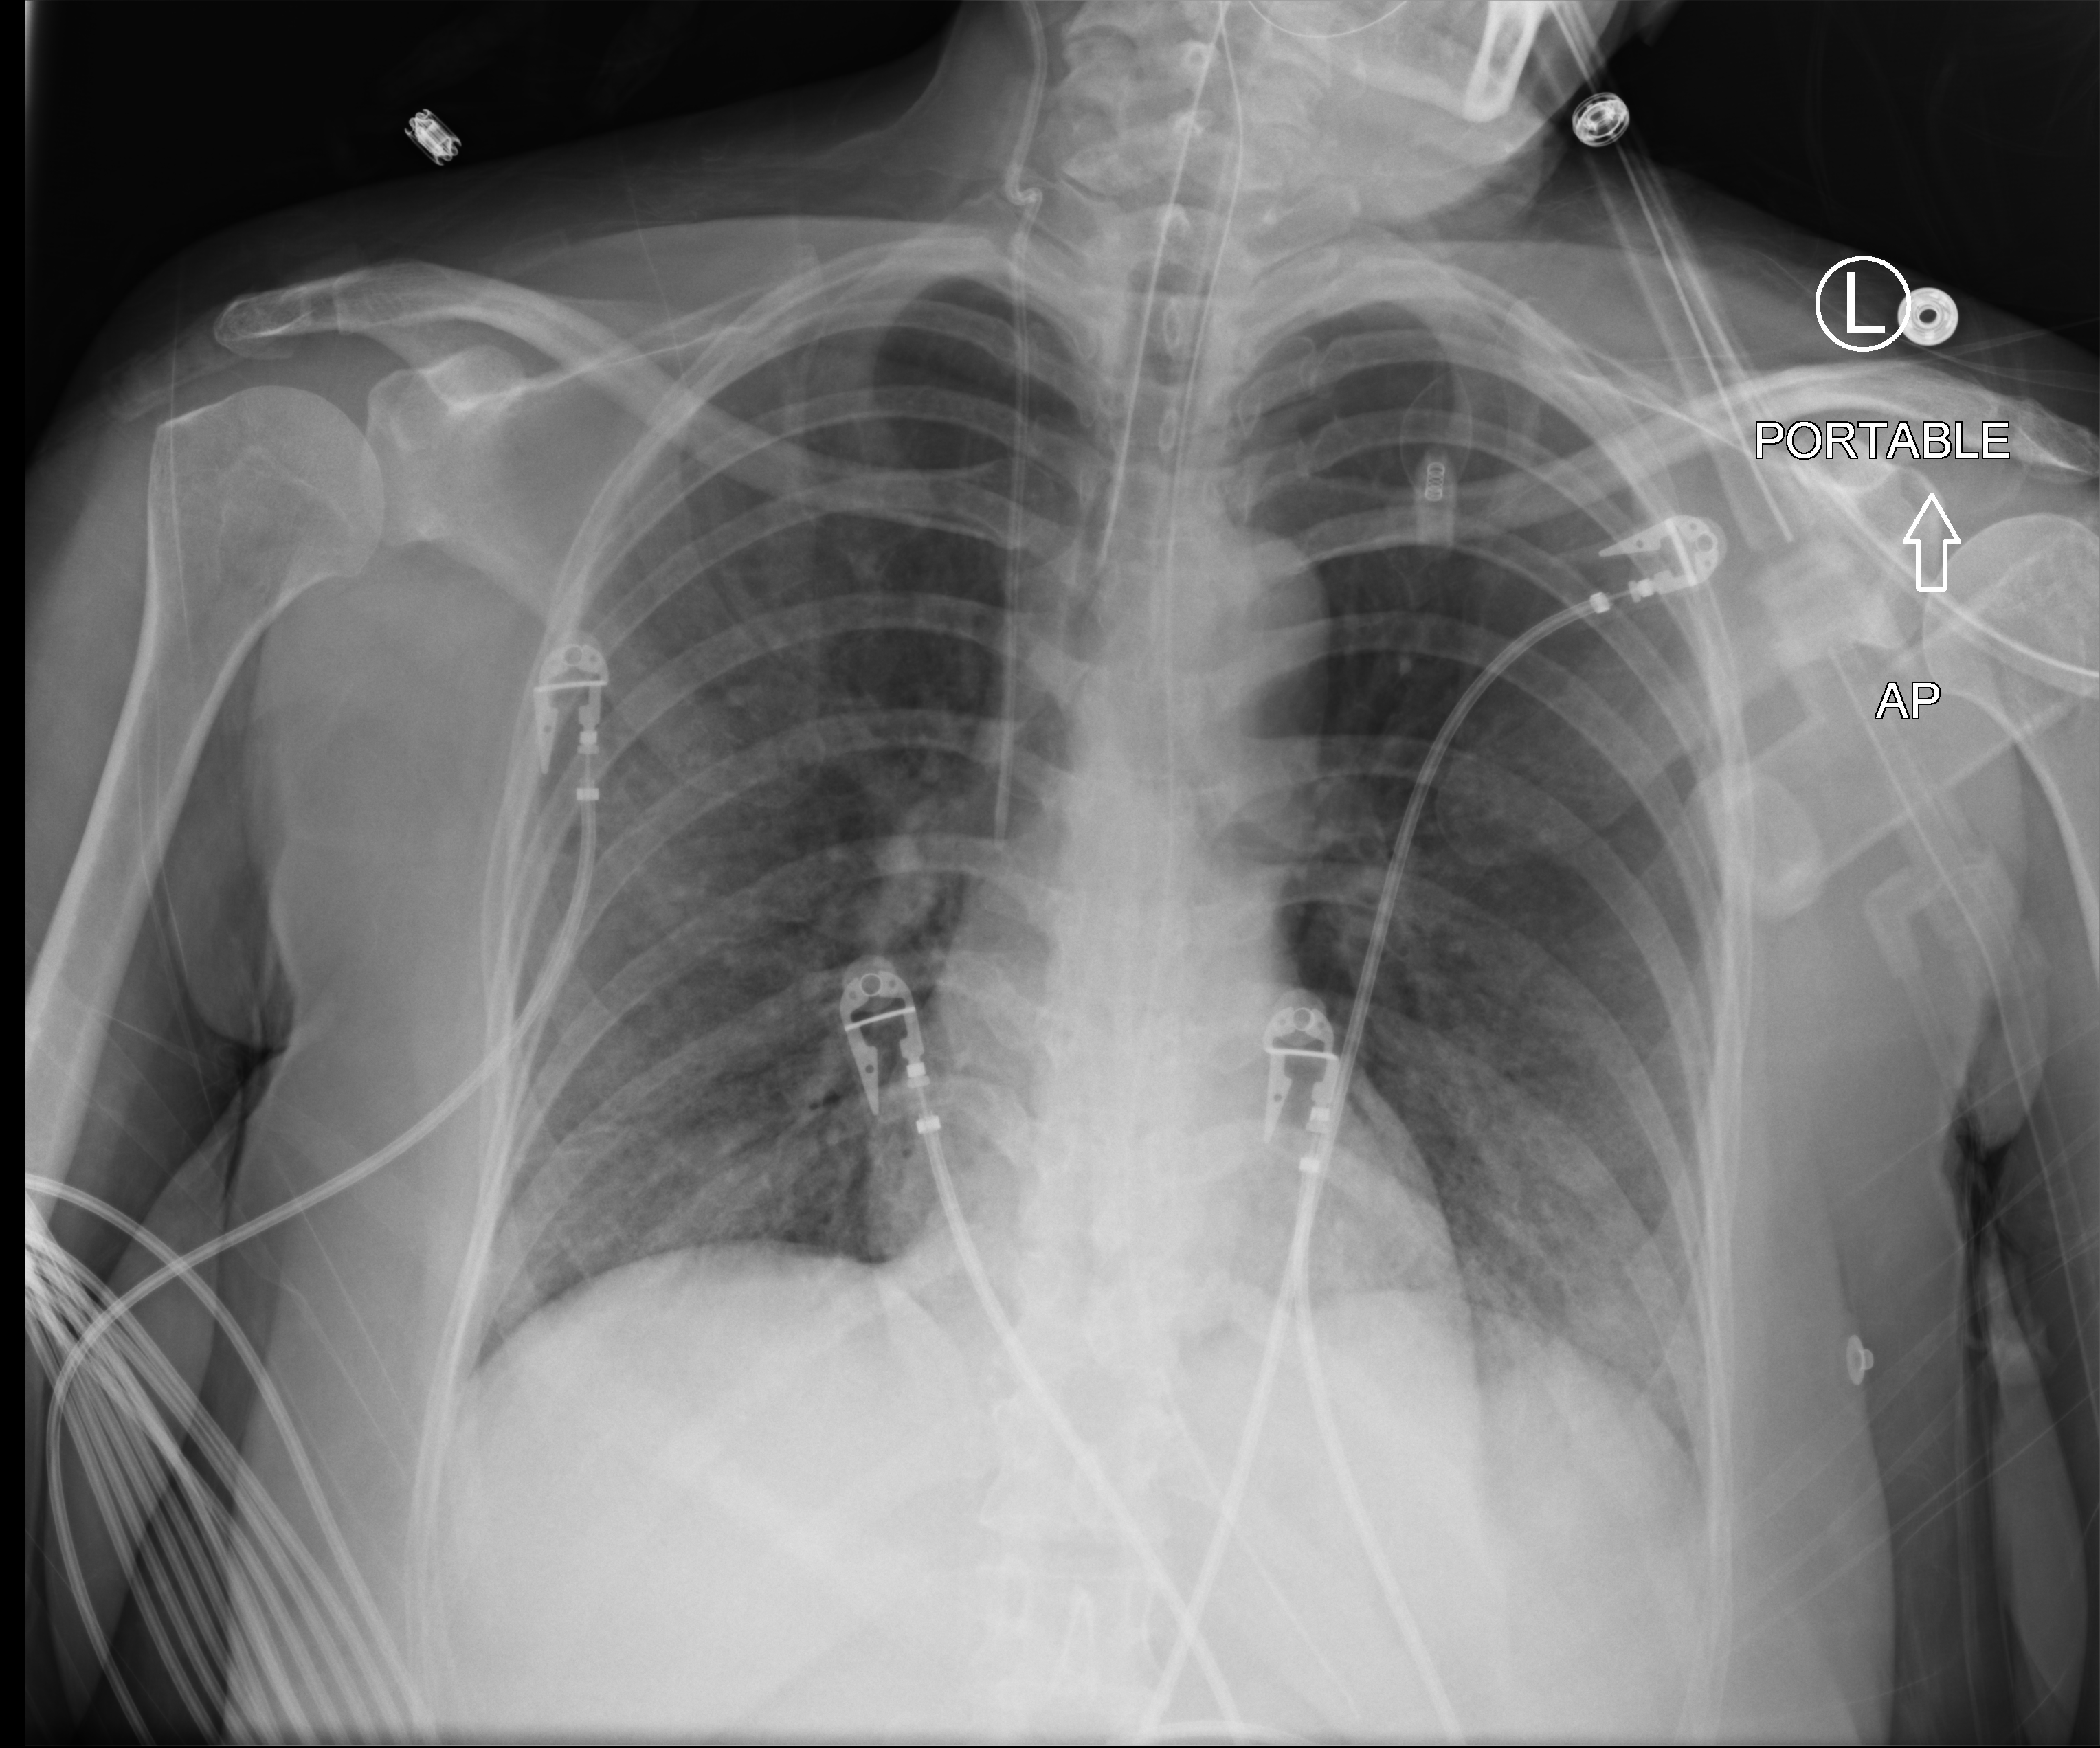
Portable chest radiograph; anteroposterior (AP) projection. Female patient hospitalised with COVID-19, age 18–59 years.
Hospital-stay facts (about this admission, not read from this image; timing relative to this image not recorded):
- hypertension (admission record): yes
- mechanically ventilated during this hospital stay: yes
- admitted to intensive care during this hospital stay: yes